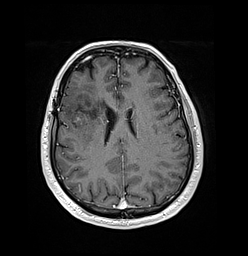
Brain MRI from a brain-tumour surgery series, one axial slice; T1-weighted post-contrast; 1 mm slice thickness; 248 × 256 image matrix, field of view 242 × 250 mm. Case-level facts recorded for this patient, not image findings: histopathology: Oligodendroglioma; WHO grade: 3; IDH mutation: yes.
Outlined on this slice (expert manual segmentation):
- tumour: bounding box <73,115,84,125> (left, top, right, bottom; pixels)